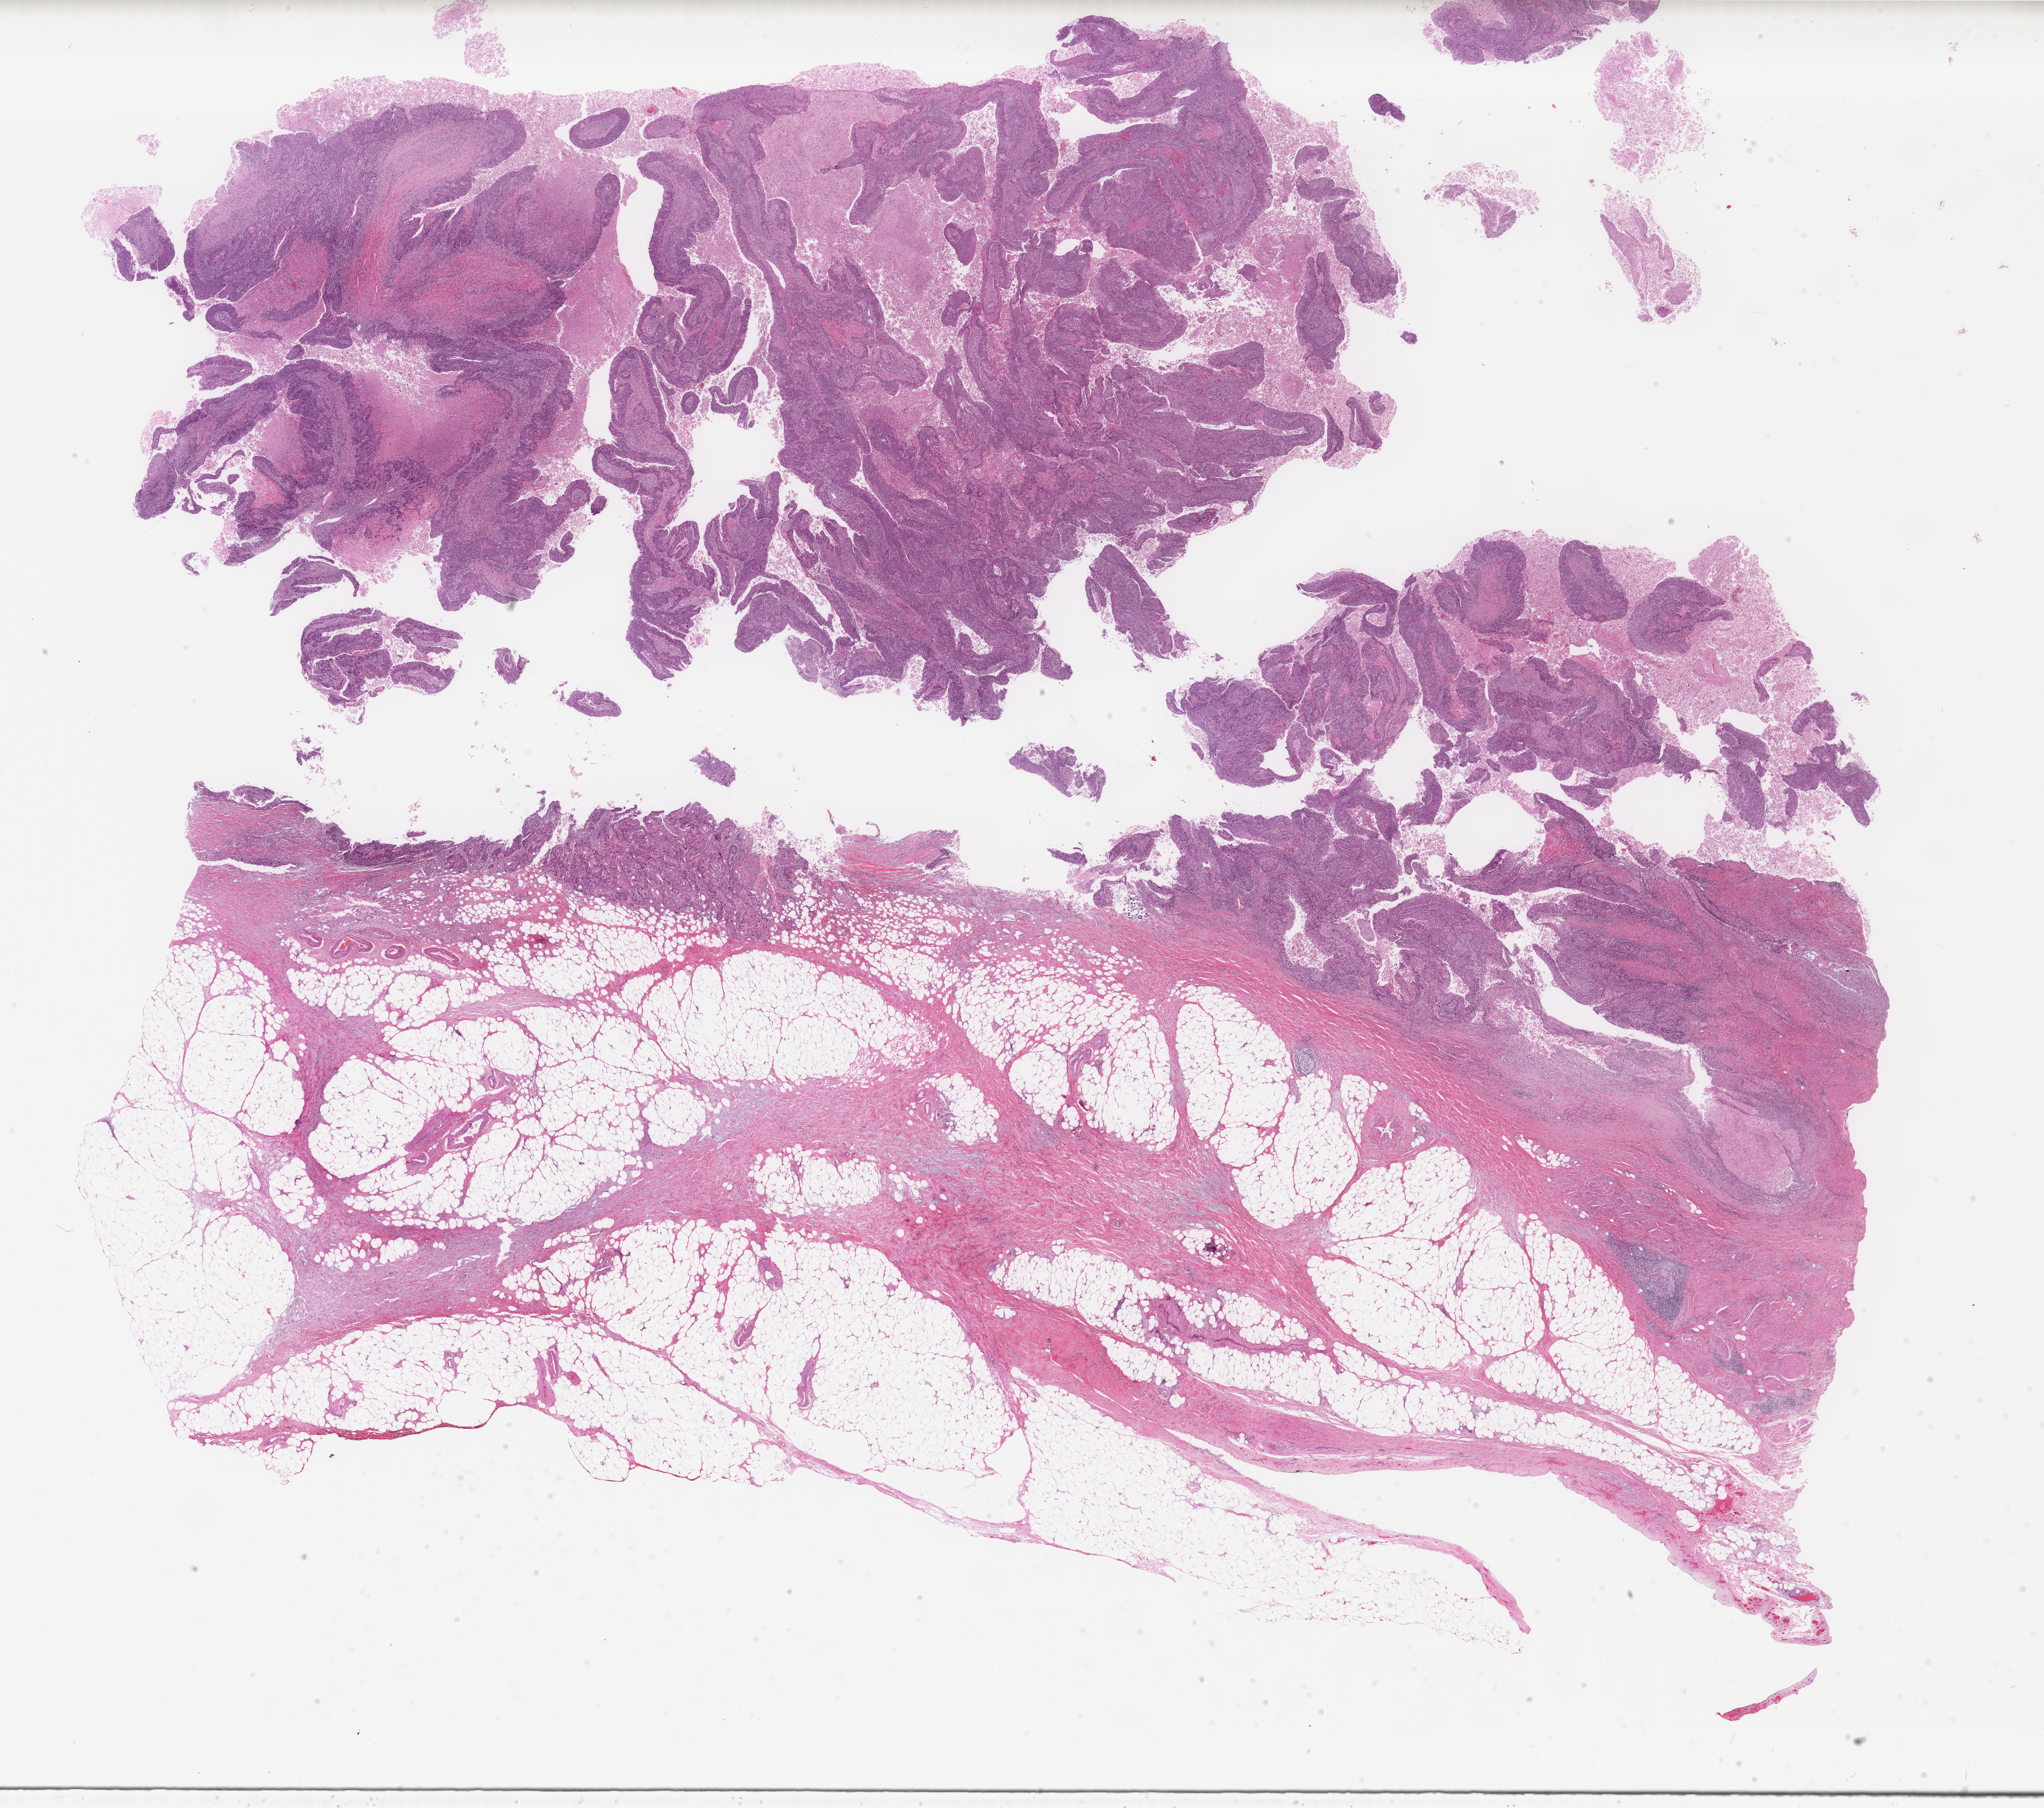
Digitized Hematoxylin and eosin (H&E) stained tissue section (whole slide) — whole scanned area (about 26.9 x 23.8 mm, acquisition: 40x scan) shown as a low-resolution overview, formalin-fixed paraffin-embedded (FFPE) diagnostic section, bladder, primary tumour sample. Male patient; age at initial diagnosis 85 years. Histologic grade: high grade.
TNM: T3b N0 M0. Histologic diagnosis: Transitional cell carcinoma. AJCC pathologic stage: II (6th edition).